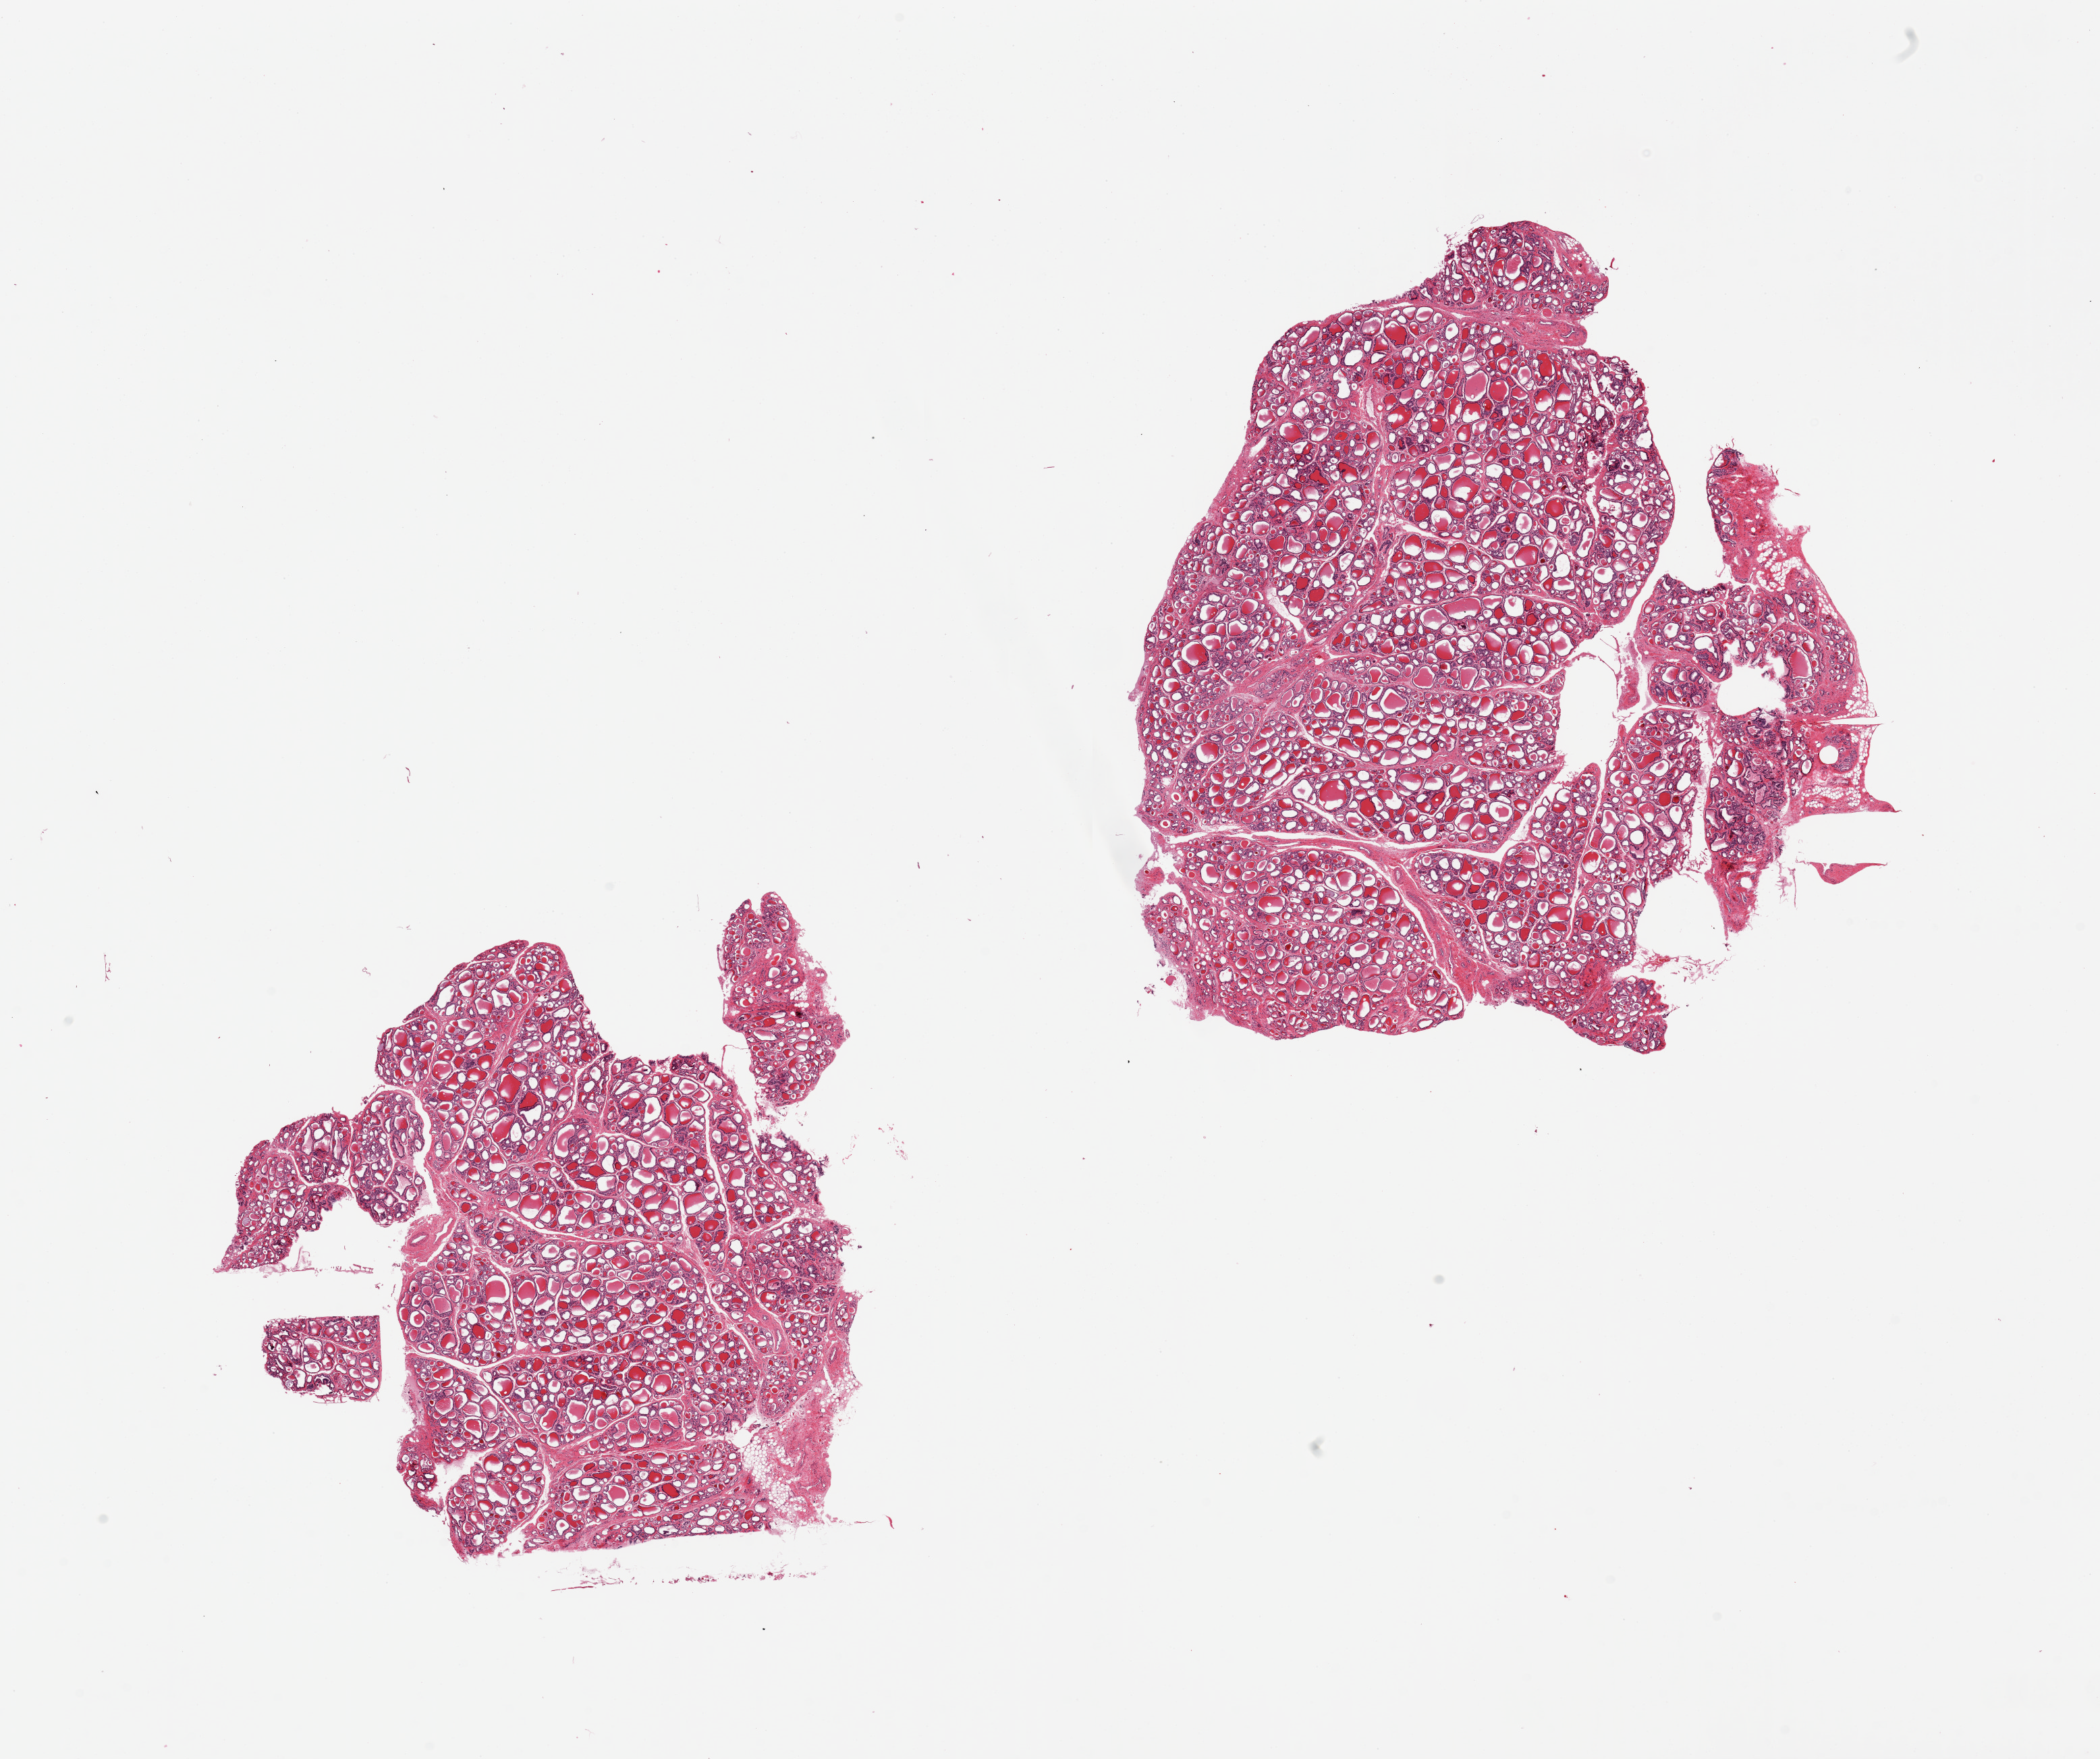
Digitized haematoxylin and eosin-stained section — shown as a low-resolution overview of the whole scanned area (about 24.6 x 20.6 mm, from a 20x scan), PAXgene-fixed, paraffin-embedded tissue, section of thyroid (target tissue), tissue donor sample. Male donor.
Reviewer comment on this tissue sample: 2 pieces, regressive changes/scarring.